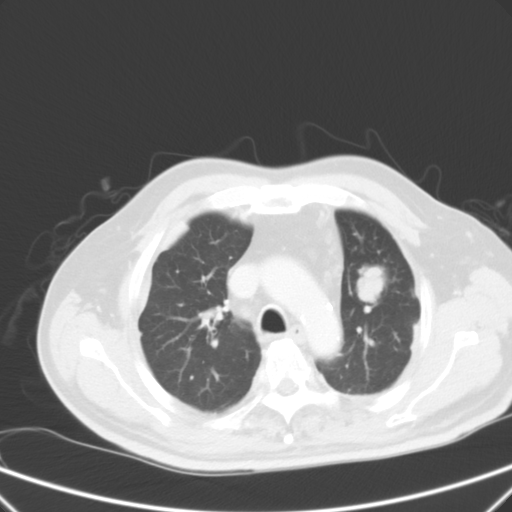
Chest CT, one axial slice. 120 kVp. Intravenous contrast given. Lung window (W 1500 / L -600 HU). 5 mm slice thickness. 512 × 512 image matrix, field of view 357 × 357 mm. Patient: male, 66 years. From the clinical record (not read from this slice): clinical TNM (as recorded): T1c N3 M1a.
Structures marked on this image (rectangle marked by the reading radiologist):
- lung tumour (recorded histology: squamous cell carcinoma): bounding box <352,264,390,307> (left, top, right, bottom; pixels)